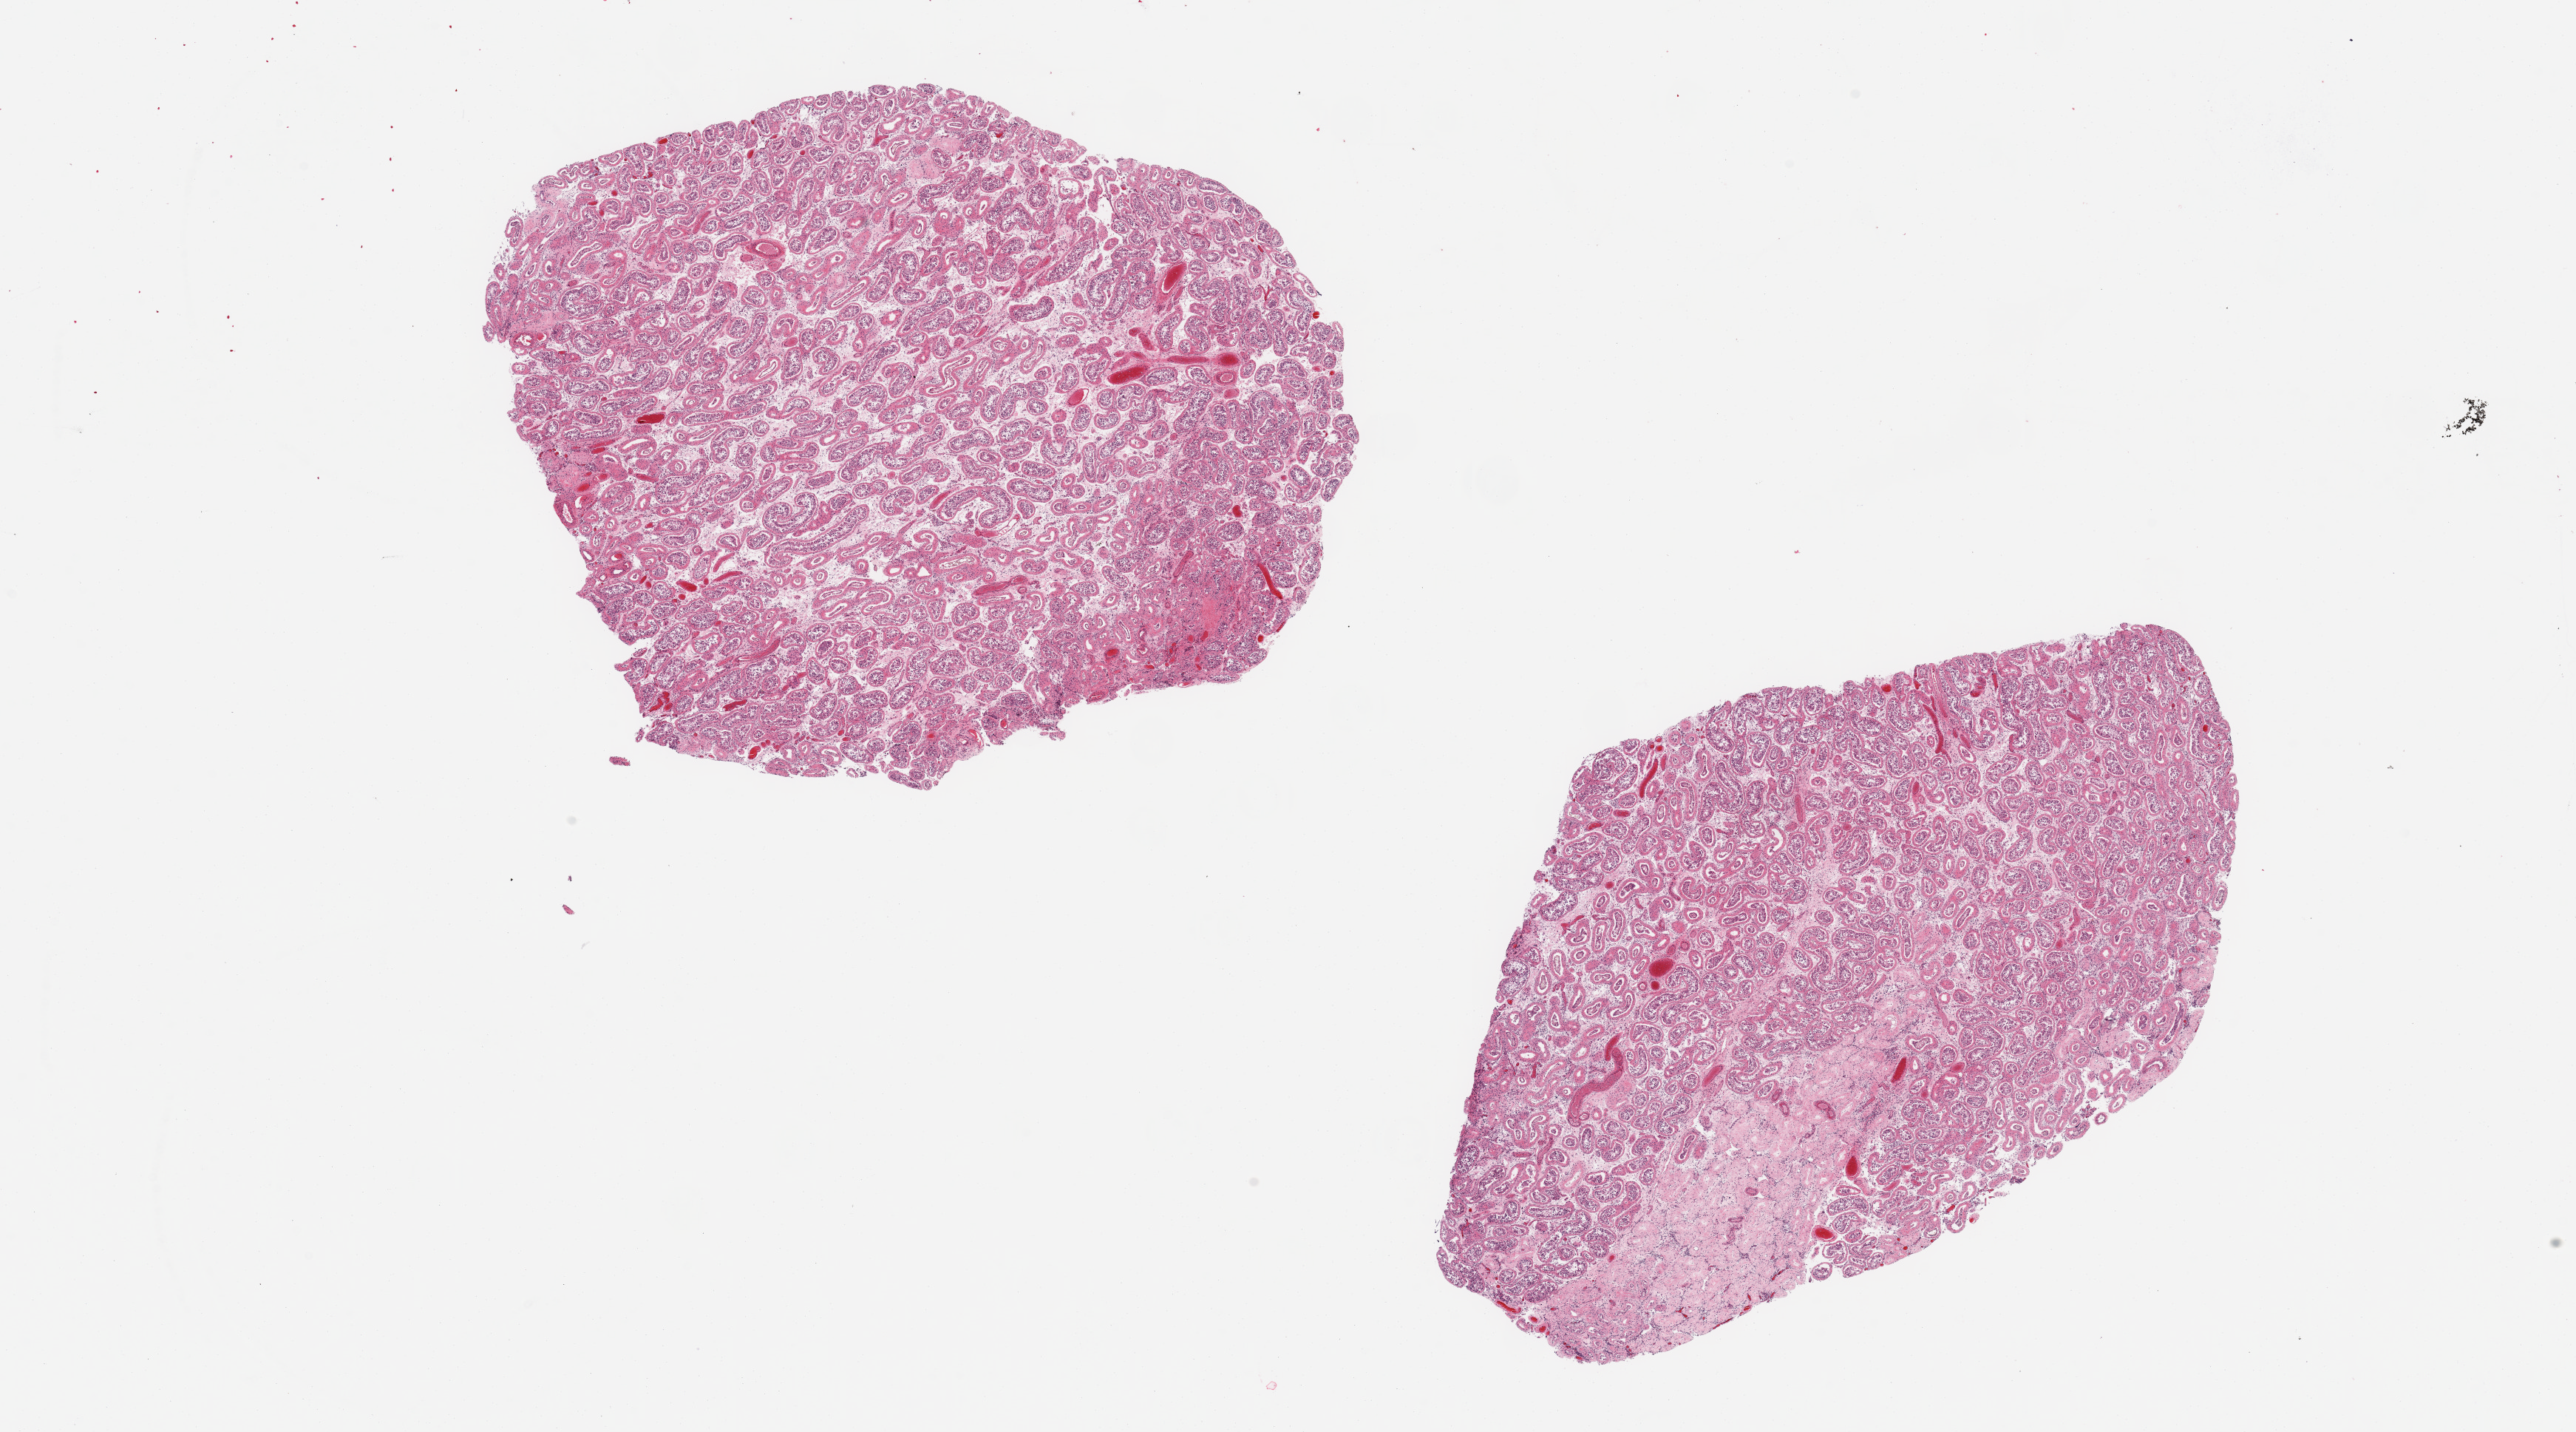
H&E whole-slide image — low-resolution overview of the scanned area, about 27.6 x 15.3 mm. PAXgene-fixed paraffin-embedded (PFPE) section. Section of testis (target tissue). Tissue donor sample. Male donor.
- pathologist's review note for this sample: 2 ~ 9x7mm pieces, a ~1x5mm scar in one aliquot. Spermatogenesis appears arrested